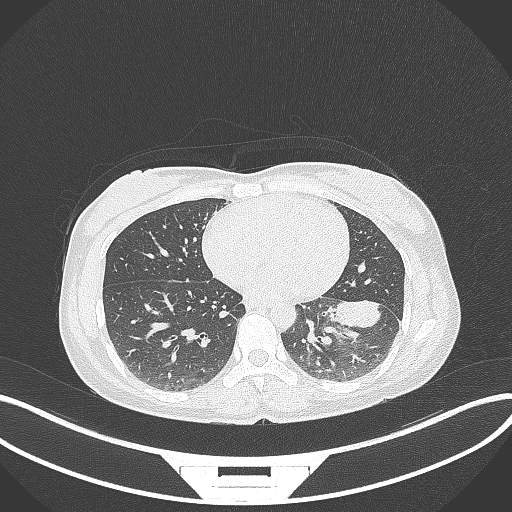
Chest CT, one axial slice. Position 26 of 244 along the scan axis. Reconstruction kernel B70f. Lung window (W 1500 / L -600 HU). 512 × 512 image matrix, field of view 400 × 400 mm. Female patient, age 41 years. Case-level facts recorded for this patient, not image findings: clinical TNM (as recorded): T2a N3 M1b.
Structures marked on this image (bounding box drawn by a radiologist):
- lung tumour (recorded histology: adenocarcinoma): bounding box (x1, y1, x2, y2) in pixels: (326, 296, 382, 336)